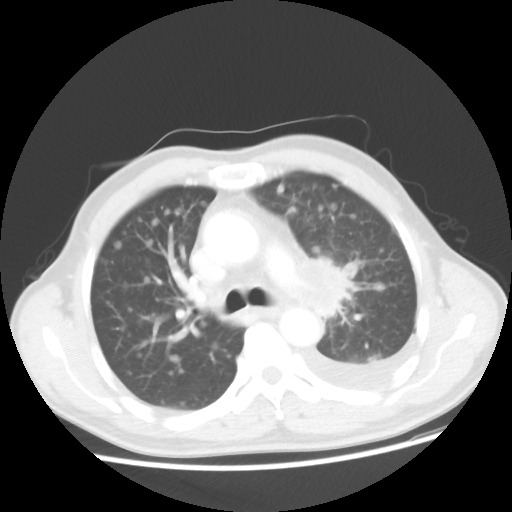
Chest CT, one axial slice. Position 31 of 48 along the scan axis. Reconstruction kernel STANDARD. 100 kVp. Lung window (W 1500 / L -600 HU). 5 mm slice thickness. 512 × 512 image matrix. Male patient, age 55 years. Case-level facts recorded for this patient, not image findings: clinical TNM (as recorded): T2 N3 M1a; histopathological grade: G3.
Annotated regions visible in this slice (rectangle marked by the reading radiologist):
- lung tumour (recorded histology: squamous cell carcinoma): box from (x=310, y=248) to (x=365, y=322) px